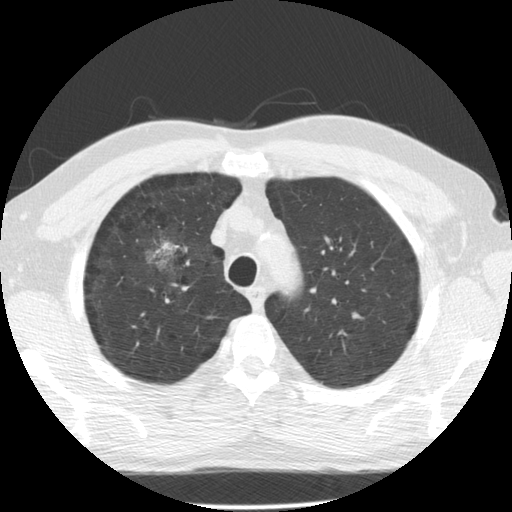
Chest CT (low-dose screening protocol), one axial image; second screening round (one year after baseline); lung window (W 1500 / L -600 HU); standard (soft-tissue) reconstruction kernel (STANDARD); 140 kVp; slice 102 of 135 in the series. Male participant, aged 60 years at enrolment. Former smoker at enrolment.
Expert reader's lesion annotation, box from (x=134, y=226) to (x=193, y=285) px. Reader record for this screening exam (exam-level; its link to the box is not recorded): non-calcified nodule or mass ≥4 mm, right upper lobe, poorly defined margins, mixed attenuation, pre-existing on the prior screen: yes; interval growth: yes. Official screen result: positive, other. Participant outcome: lung cancer diagnosed 562 days after this screen — papillary adenocarcinoma, NOS, right upper lobe, moderately differentiated (G2), stage IB (AJCC 6th edition), 32 mm at pathology.